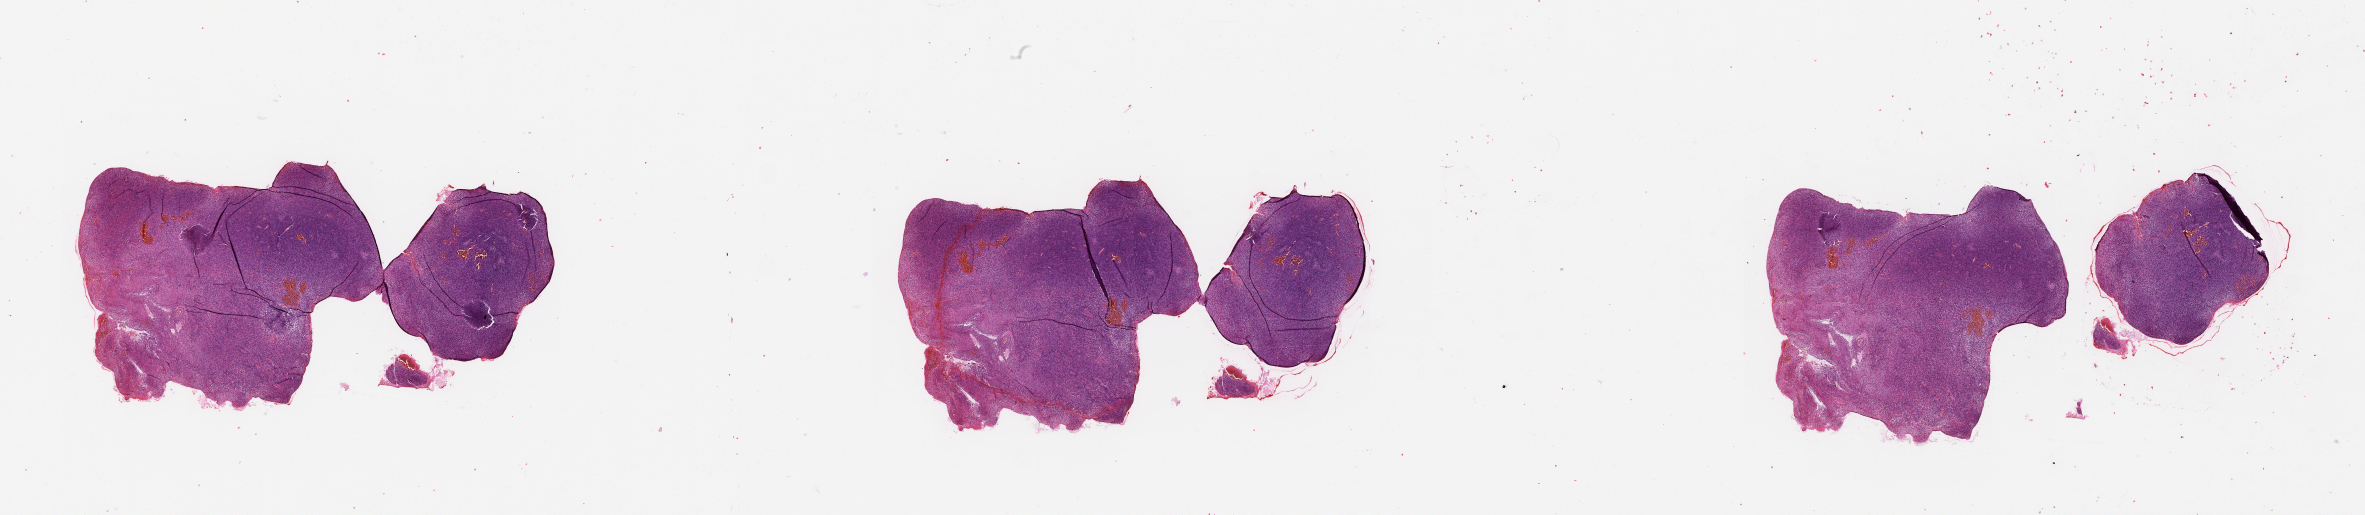
H&E whole-slide image, a low-resolution overview of the entire scanned area, about 38.1 x 8.3 mm (acquisition: 20x scan), tumour tissue sample, sampled site: occipital cortex. Patient: female, age 37 years. Pathologist review of this section (percent, as recorded): tumour nuclei 85%, necrosis 10%.
Diagnosis: Glioblastoma. Primary tumour site (as recorded): occipital lobe.